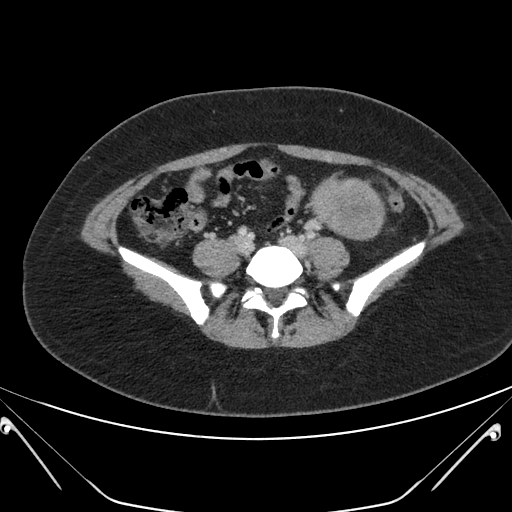
Contrast-enhanced abdominal CT, one axial slice. Position 66 of 168 along the scan axis. 120 kVp. Intravenous contrast given. Soft-tissue window (W 400 / L 40 HU). 3 mm slice thickness. 512 × 512 image matrix, field of view 394 × 394 mm. Patient: female, 26 years. Case-level facts recorded for this patient, not image findings: diagnosis: adrenocortical carcinoma; tumour side: left adrenal; tumour size at pathology: 28 cm.
Annotated regions visible in this slice (semi-automatically segmented with operator editing):
- mass: bounding box [x1, y1, x2, y2] px = [313, 181, 382, 238]